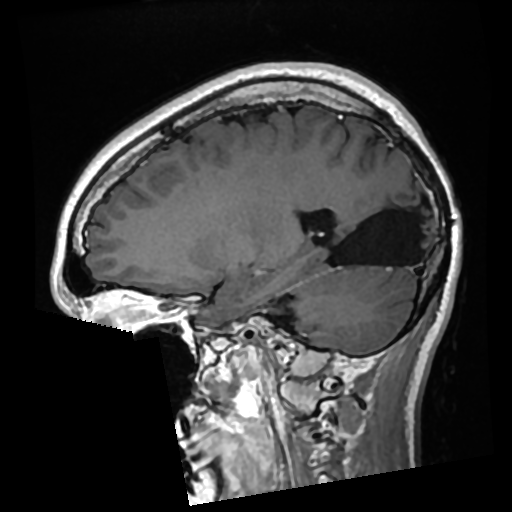
Brain MRI from a brain-tumour surgery series, one sagittal slice. Position 108 of 276 along the scan axis. T1-weighted post-contrast. 512 × 512 image matrix, field of view 250 × 250 mm. Case-level facts recorded for this patient, not image findings: histopathology: Glioma with ependymal features; WHO grade: 2; tumour location: Left Parietal.
Annotated regions visible in this slice (outlined manually by an expert reader):
- previous resection cavity: box from (x=329, y=186) to (x=422, y=266) px